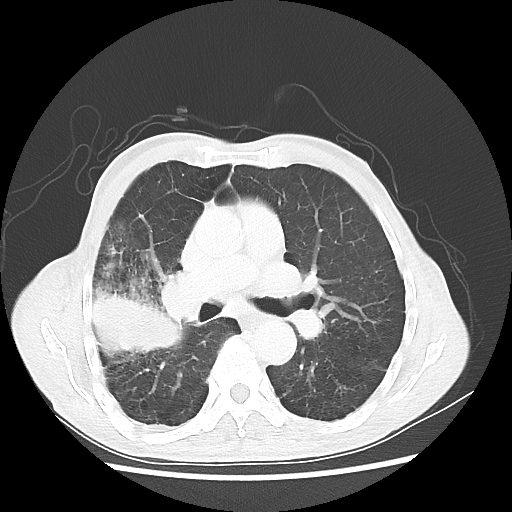
Chest CT, one axial slice. Slice 30 of 58 in the series (ordered by position). 100 kVp. Lung window (W 1500 / L -600 HU). 512 × 512 image matrix, field of view 351 × 351 mm. Male patient, age 75 years. From the clinical record (not read from this slice): clinical TNM (as recorded): T4 N1 M1.
Outlined on this slice (bounding box drawn by a radiologist):
- lung tumour (recorded histology: adenocarcinoma): bounding box <87,282,183,357> (left, top, right, bottom; pixels)